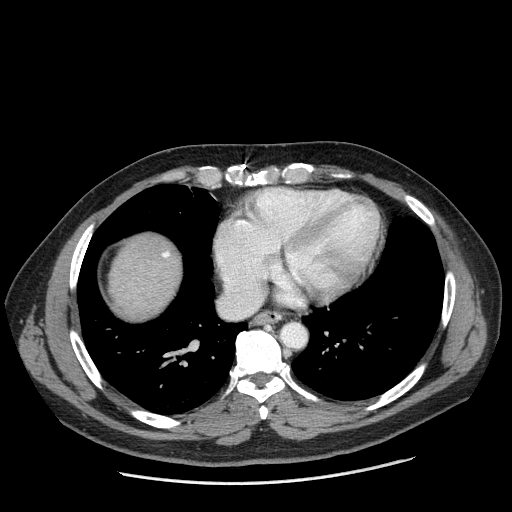
Contrast-enhanced abdominal CT (liver protocol), one axial slice; position 181 of 198 along the scan axis; reconstruction kernel STANDARD; 120 kVp; one of 2 acquisitions stored at this slice position; soft-tissue window (W 400 / L 40 HU); 2.5 mm slice thickness; 512 × 512 image matrix. Case-level facts recorded for this patient, not image findings: diagnosis: hepatocellular carcinoma (patient treated with transarterial chemoembolisation; whether this scan precedes or follows treatment is not stated here); TNM stage (as recorded): Stage-II; Child-Pugh class: A; tumour differentiation: moderately differentiated; tumour size: 2.6 cm.
Annotated regions visible in this slice (semi-automatic segmentation, software-assisted and operator-edited):
- liver parenchyma outside the tumour (the mass and vessels are separate outlines, so this box may not span the whole liver): bounding box <110,234,180,318> (left, top, right, bottom; pixels)
- liver vessels: <162,252,170,258>